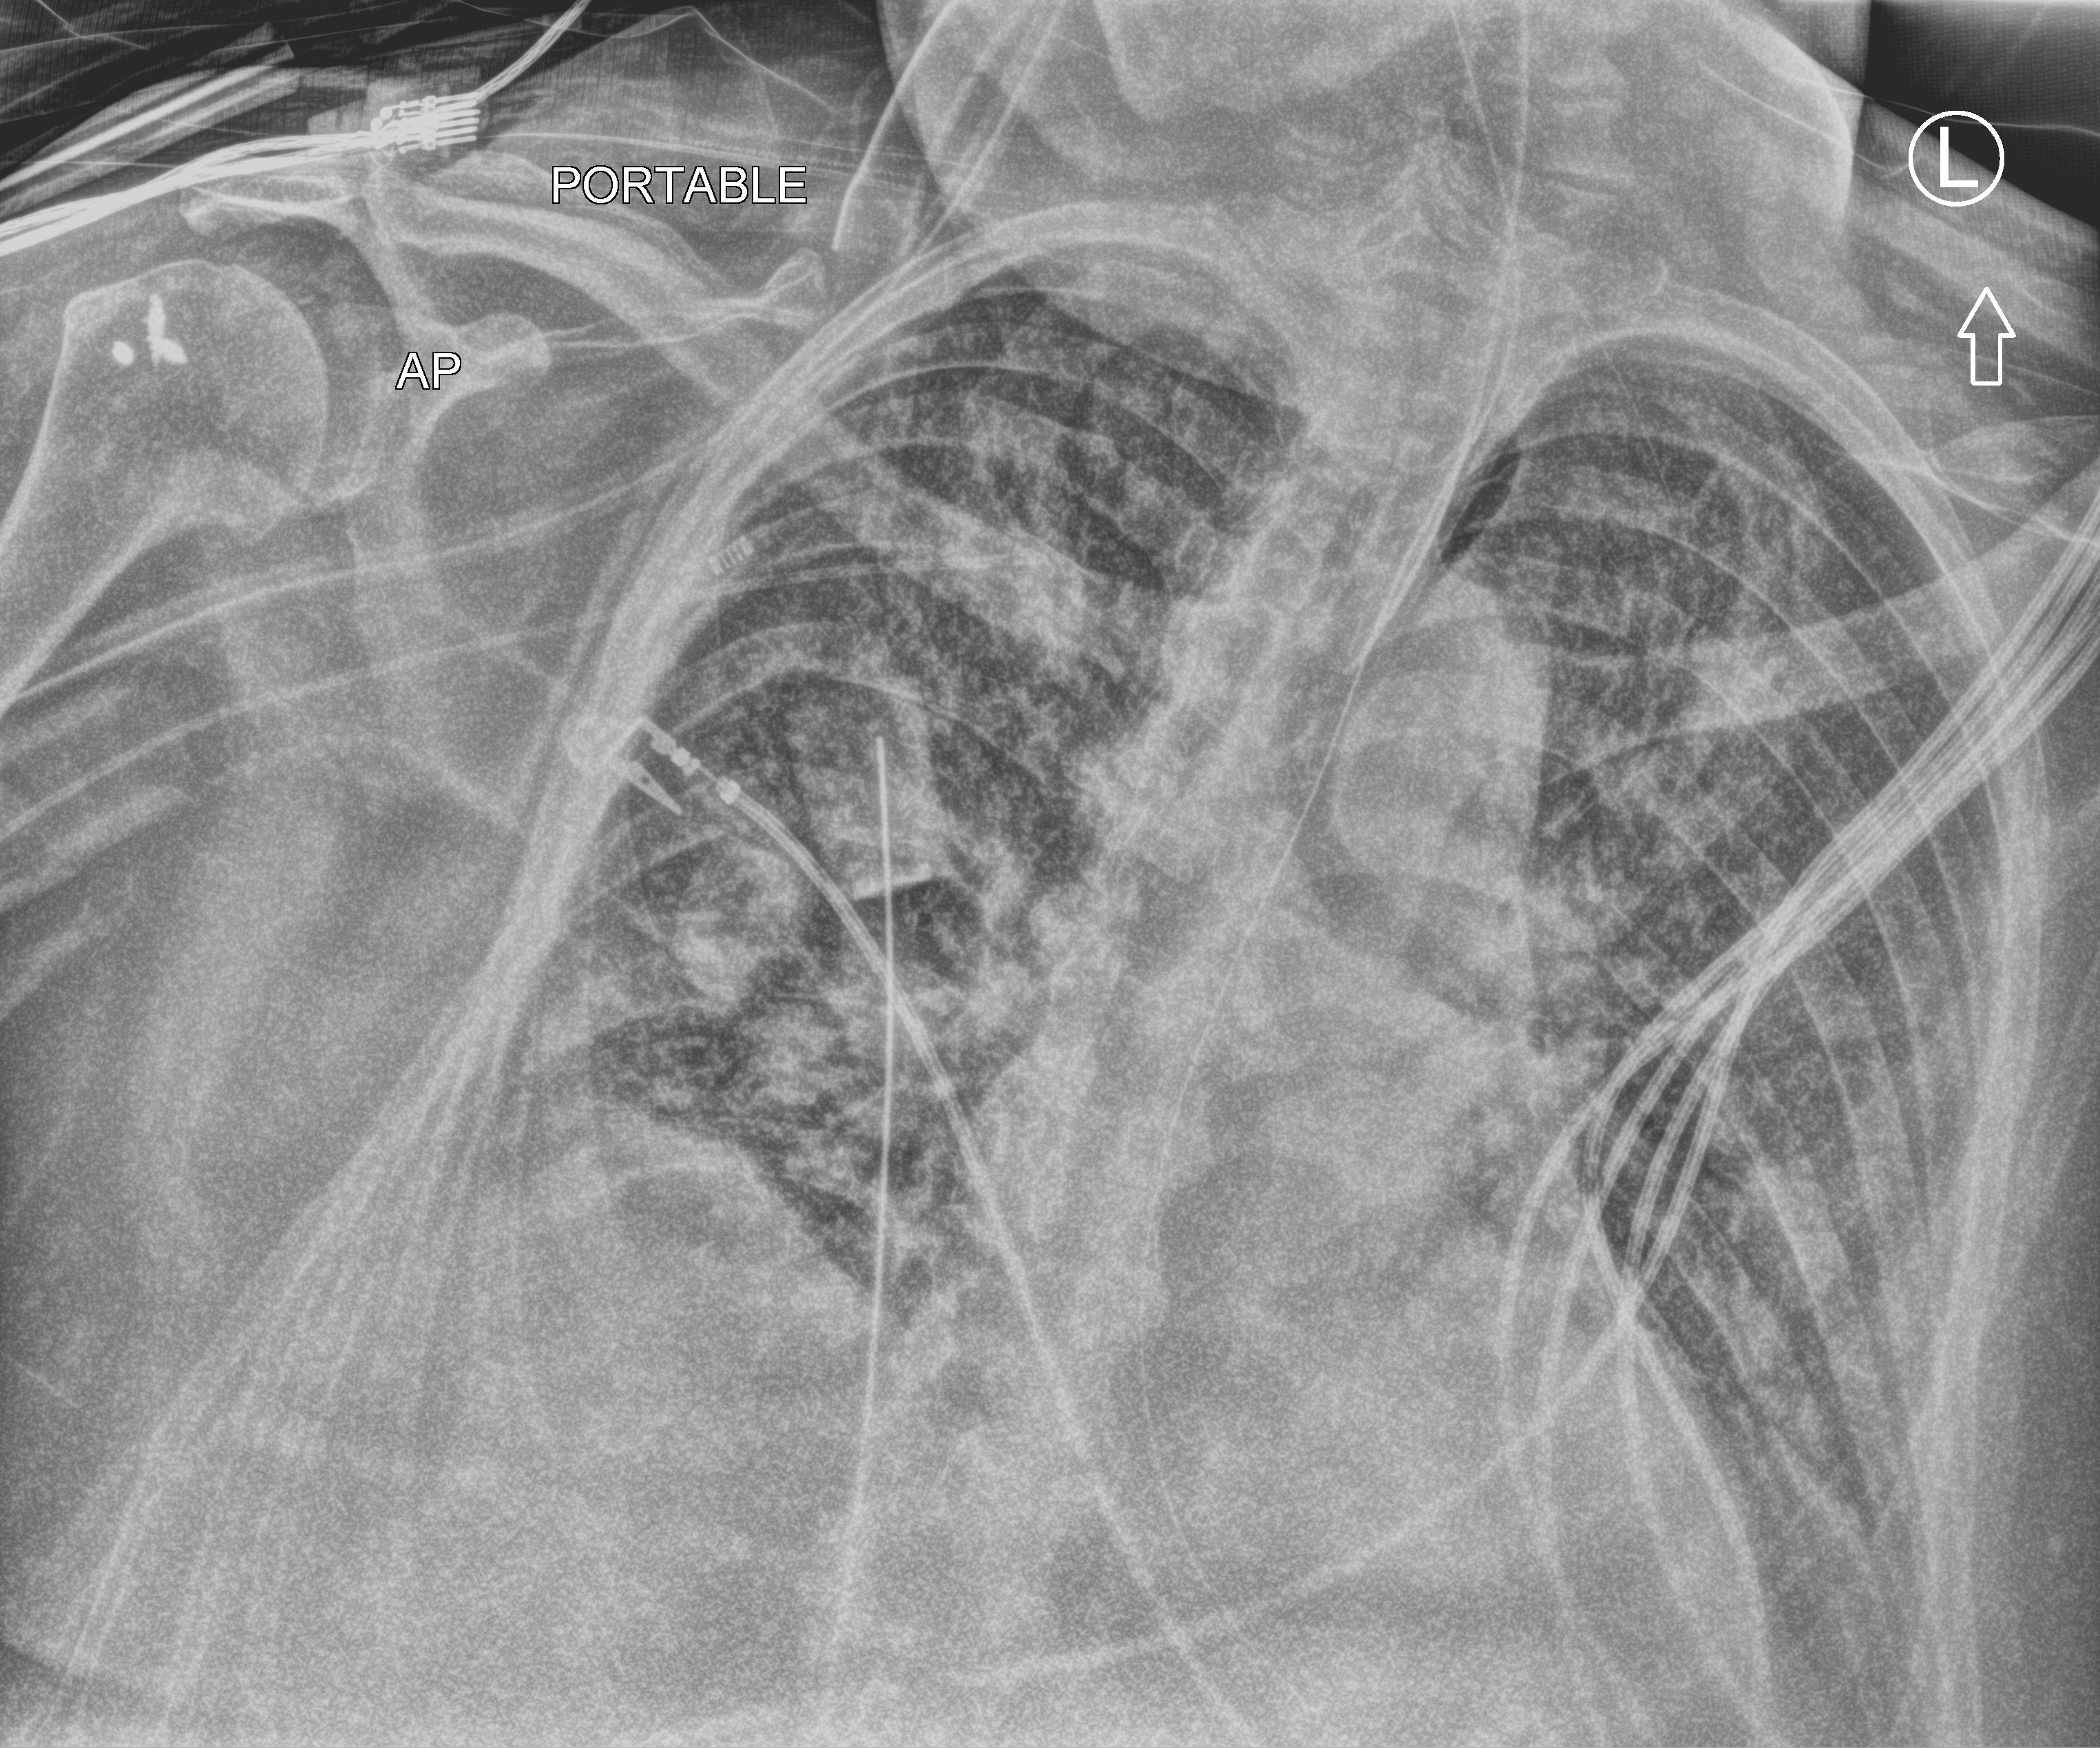
Bedside chest radiograph (computed radiography), anteroposterior (AP) projection. Male patient hospitalised with COVID-19, age 60–74 years.
From the hospital-stay record, not from the radiograph (when in the stay this image was taken is not recorded): admitted to intensive care during this hospital stay: yes; smoking status (admission record): former.